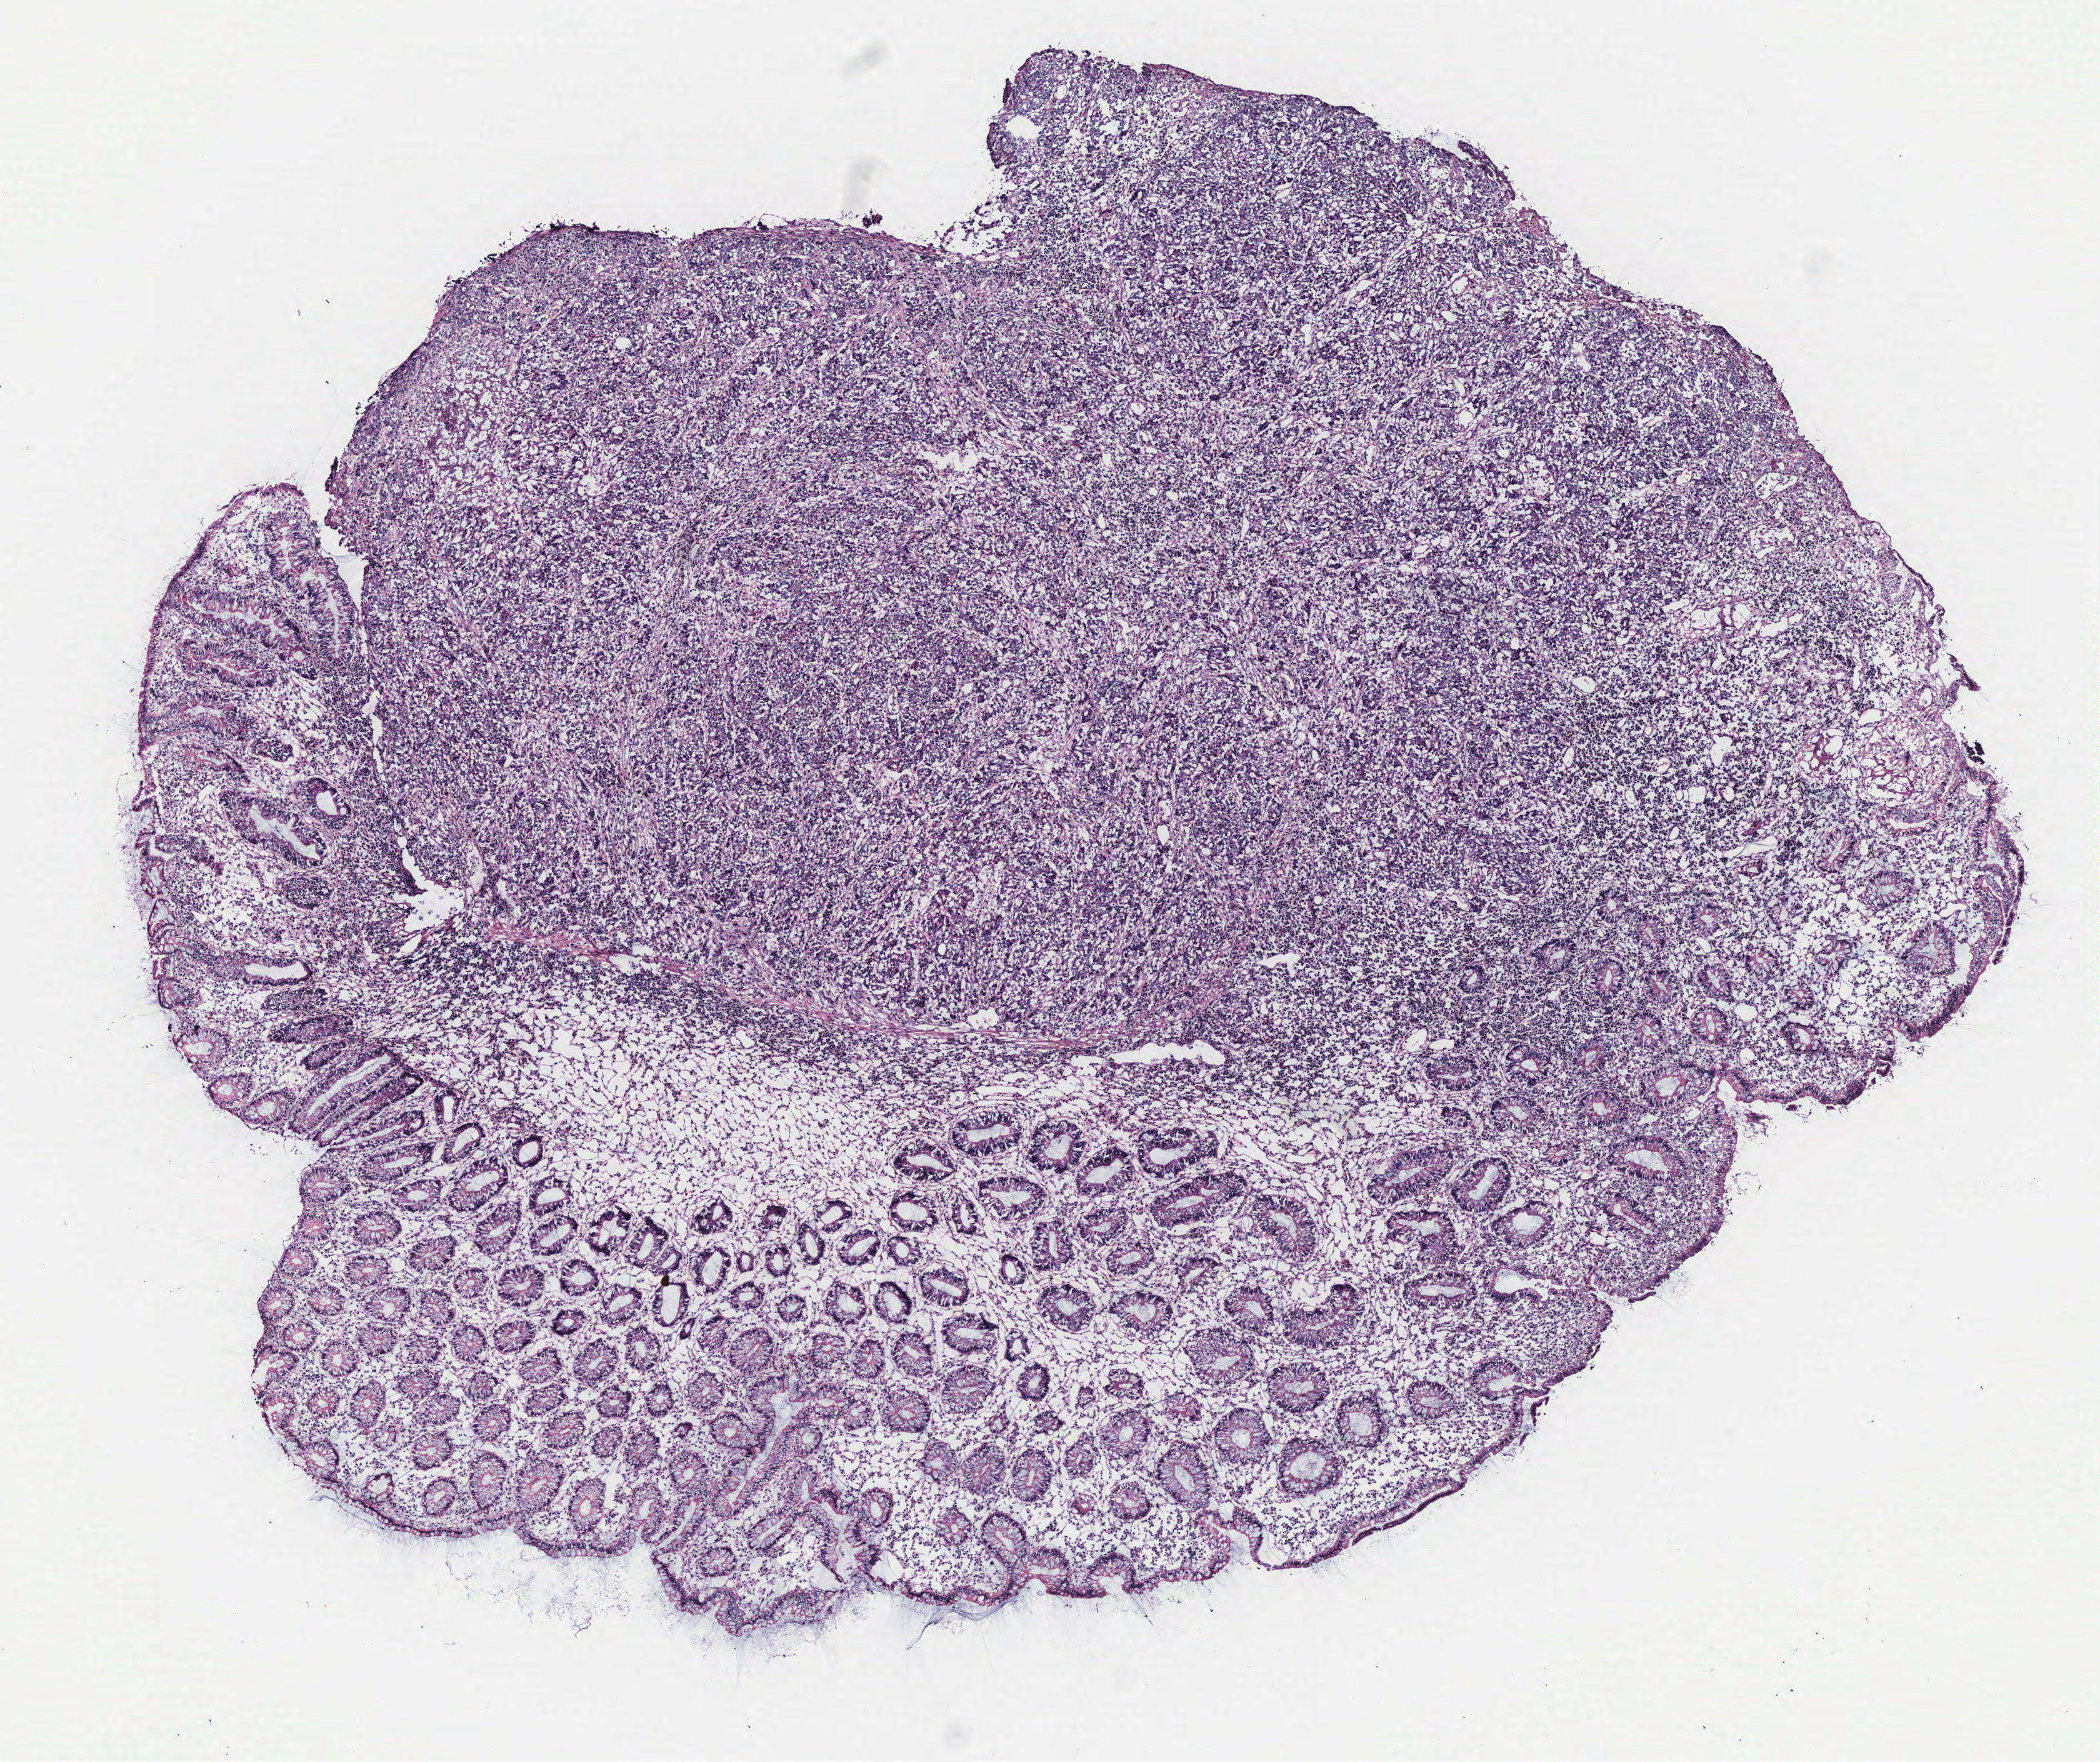
Digitized H&E tissue section (whole slide) — a low-resolution overview of the entire scanned area, about 6.7 x 5.6 mm; normal (non-tumour) tissue sample, colon. Female, 73 y/o.
This section: normal (non-tumour) tissue from the same patient. Patient diagnosis: Adenocarcinoma, NOS.